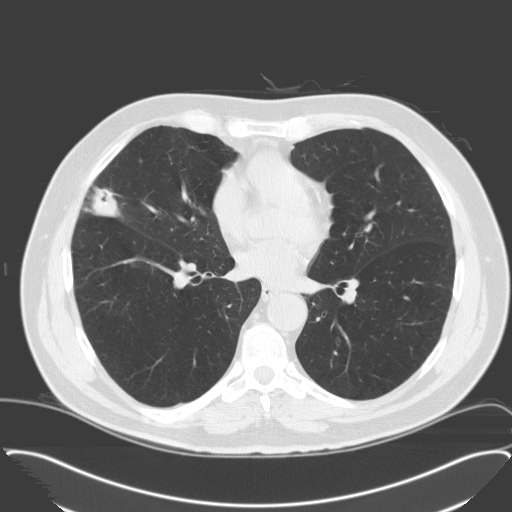
Low-dose screening chest CT, one axial slice. 120 kVp. Lung window (W 1500 / L -600 HU). 3.2 mm slice thickness. 512 × 512 image matrix, field of view 400 × 400 mm.
Structures marked on this image (expert manual segmentation):
- lesion 1 (tumor, middle lobe of right lung): box from (x=92, y=188) to (x=120, y=217) px